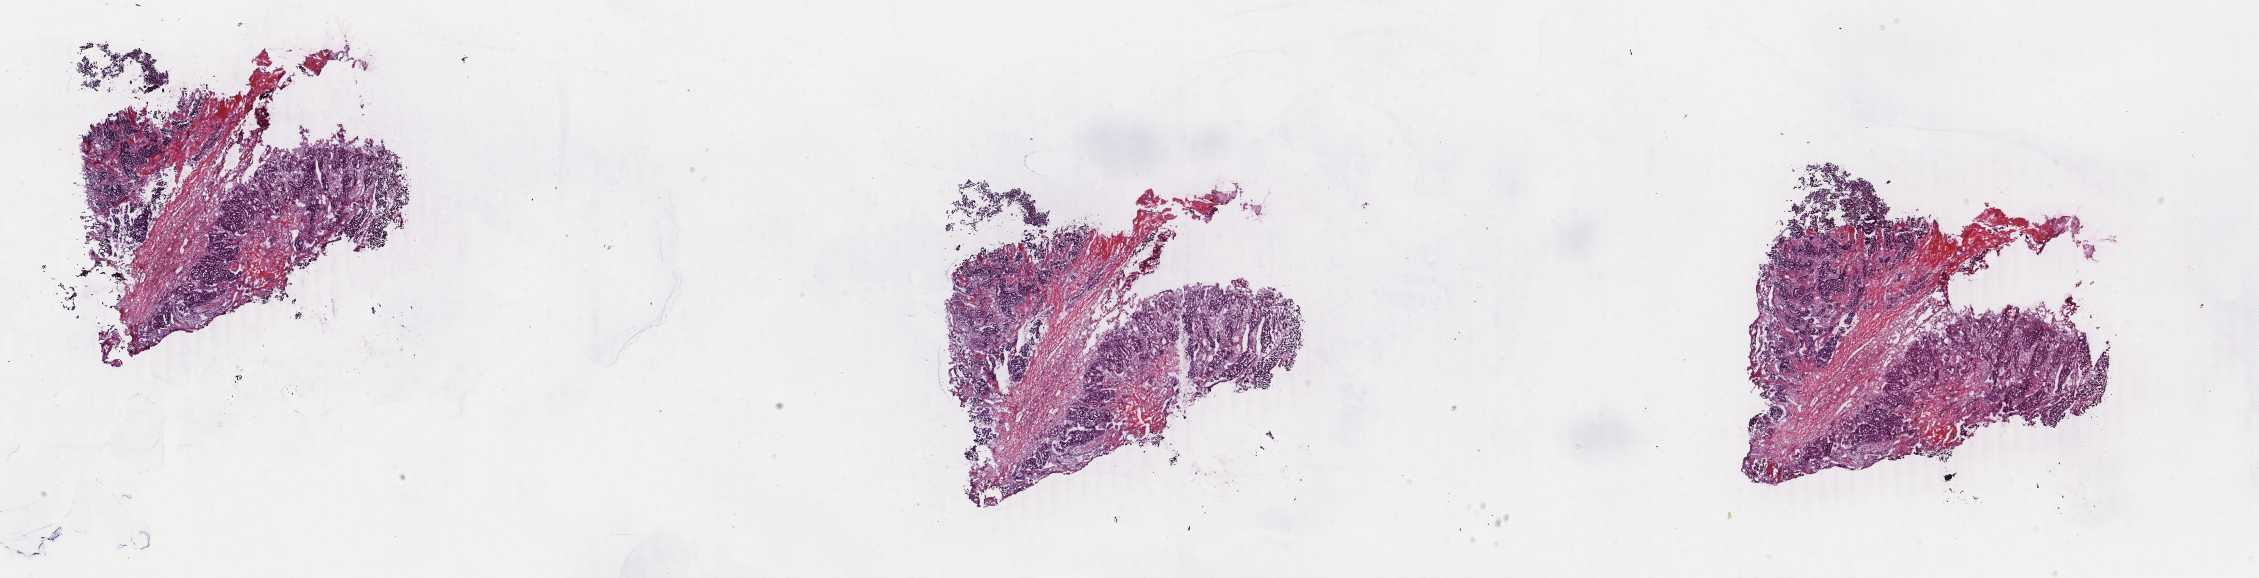
Digitized H&E-stained tissue section (whole slide), whole scanned area (about 35.9 x 9.2 mm, acquisition: 40x scan) shown as a low-resolution overview. Frozen section from the bottom of the tissue portion. Primary tumour sample from the breast. Female, age 75 years at initial diagnosis. Slide review estimates, as recorded: tumour cells 80%, tumour nuclei 80%, normal cells 0%, stromal cells 20%, necrosis 0%. Infiltration values recorded for this section: lymphocyte infiltration 1%, monocyte infiltration 0%, neutrophil infiltration 0%.
- AJCC pathologic stage: IIB
- lymph nodes positive (case pathology): 0 of 9 examined
- pathologic diagnosis: Infiltrating duct mixed with other types of carcinoma